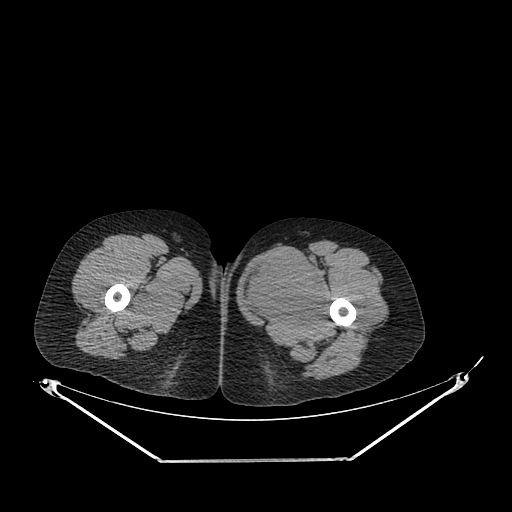
CT of an extremity soft-tissue mass (from a PET/CT study), one axial slice. Position 246 of 267 along the scan axis. Reconstruction kernel SOFT. 120 kVp. Soft-tissue window (W 400 / L 40 HU). 512 × 512 image matrix, field of view 500 × 500 mm. Female patient. Case-level facts recorded for this patient, not image findings: histological type: pleiomorphic leiomyosarcoma; grade: intermediate; site of the primary tumour: left thigh.
Annotated regions visible in this slice (expert contour drawn on MRI and transferred to this co-registered scan by the dataset authors):
- gross tumour volume including surrounding oedema: bounding box [x1, y1, x2, y2] px = [240, 256, 327, 325]
- gross tumour volume (mass): [240, 258, 327, 325]